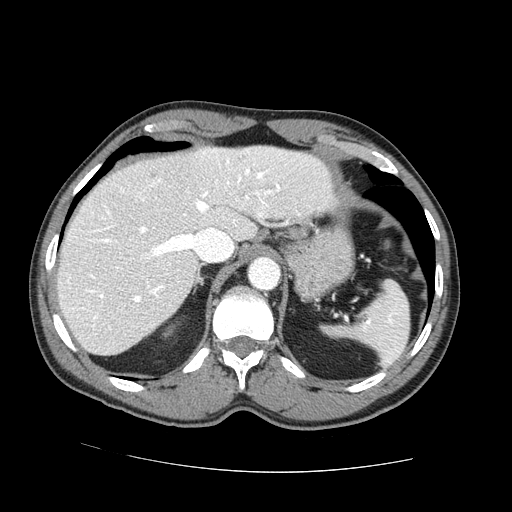
Contrast-enhanced abdominal CT (liver protocol), one axial slice. Position 54 of 73 along the scan axis. One of 2 acquisitions stored at this slice position. Soft-tissue window (W 400 / L 40 HU). 512 × 512 image matrix, field of view 380 × 380 mm. Case-level facts recorded for this patient, not image findings: diagnosis: hepatocellular carcinoma (patient treated with transarterial chemoembolisation; whether this scan precedes or follows treatment is not stated here); TNM stage (as recorded): Stage-IVA.
Structures marked on this image (semi-automatic segmentation, software-assisted and operator-edited):
- liver parenchyma outside the tumour (the mass and vessels are separate outlines, so this box may not span the whole liver): box from (x=56, y=146) to (x=334, y=354) px
- liver vessels: (x=82, y=150)–(x=280, y=327)